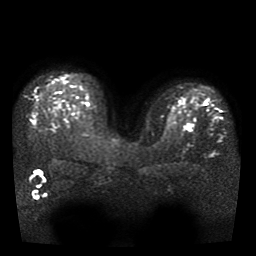
Breast MRI, one axial slice; slice 27 of 41 in the series (ordered by position); diffusion-weighted series; image 2 of 4 stored at this slice position (different b-values; order by instance number); 1.5 T; 5 mm slice thickness; 256 × 256 image matrix, field of view 330 × 330 mm. Female patient.
Structures marked on this image (outlined manually by an expert reader):
- tumour on diffusion-weighted imaging: bounding box (x1, y1, x2, y2) in pixels: (189, 125, 195, 129)